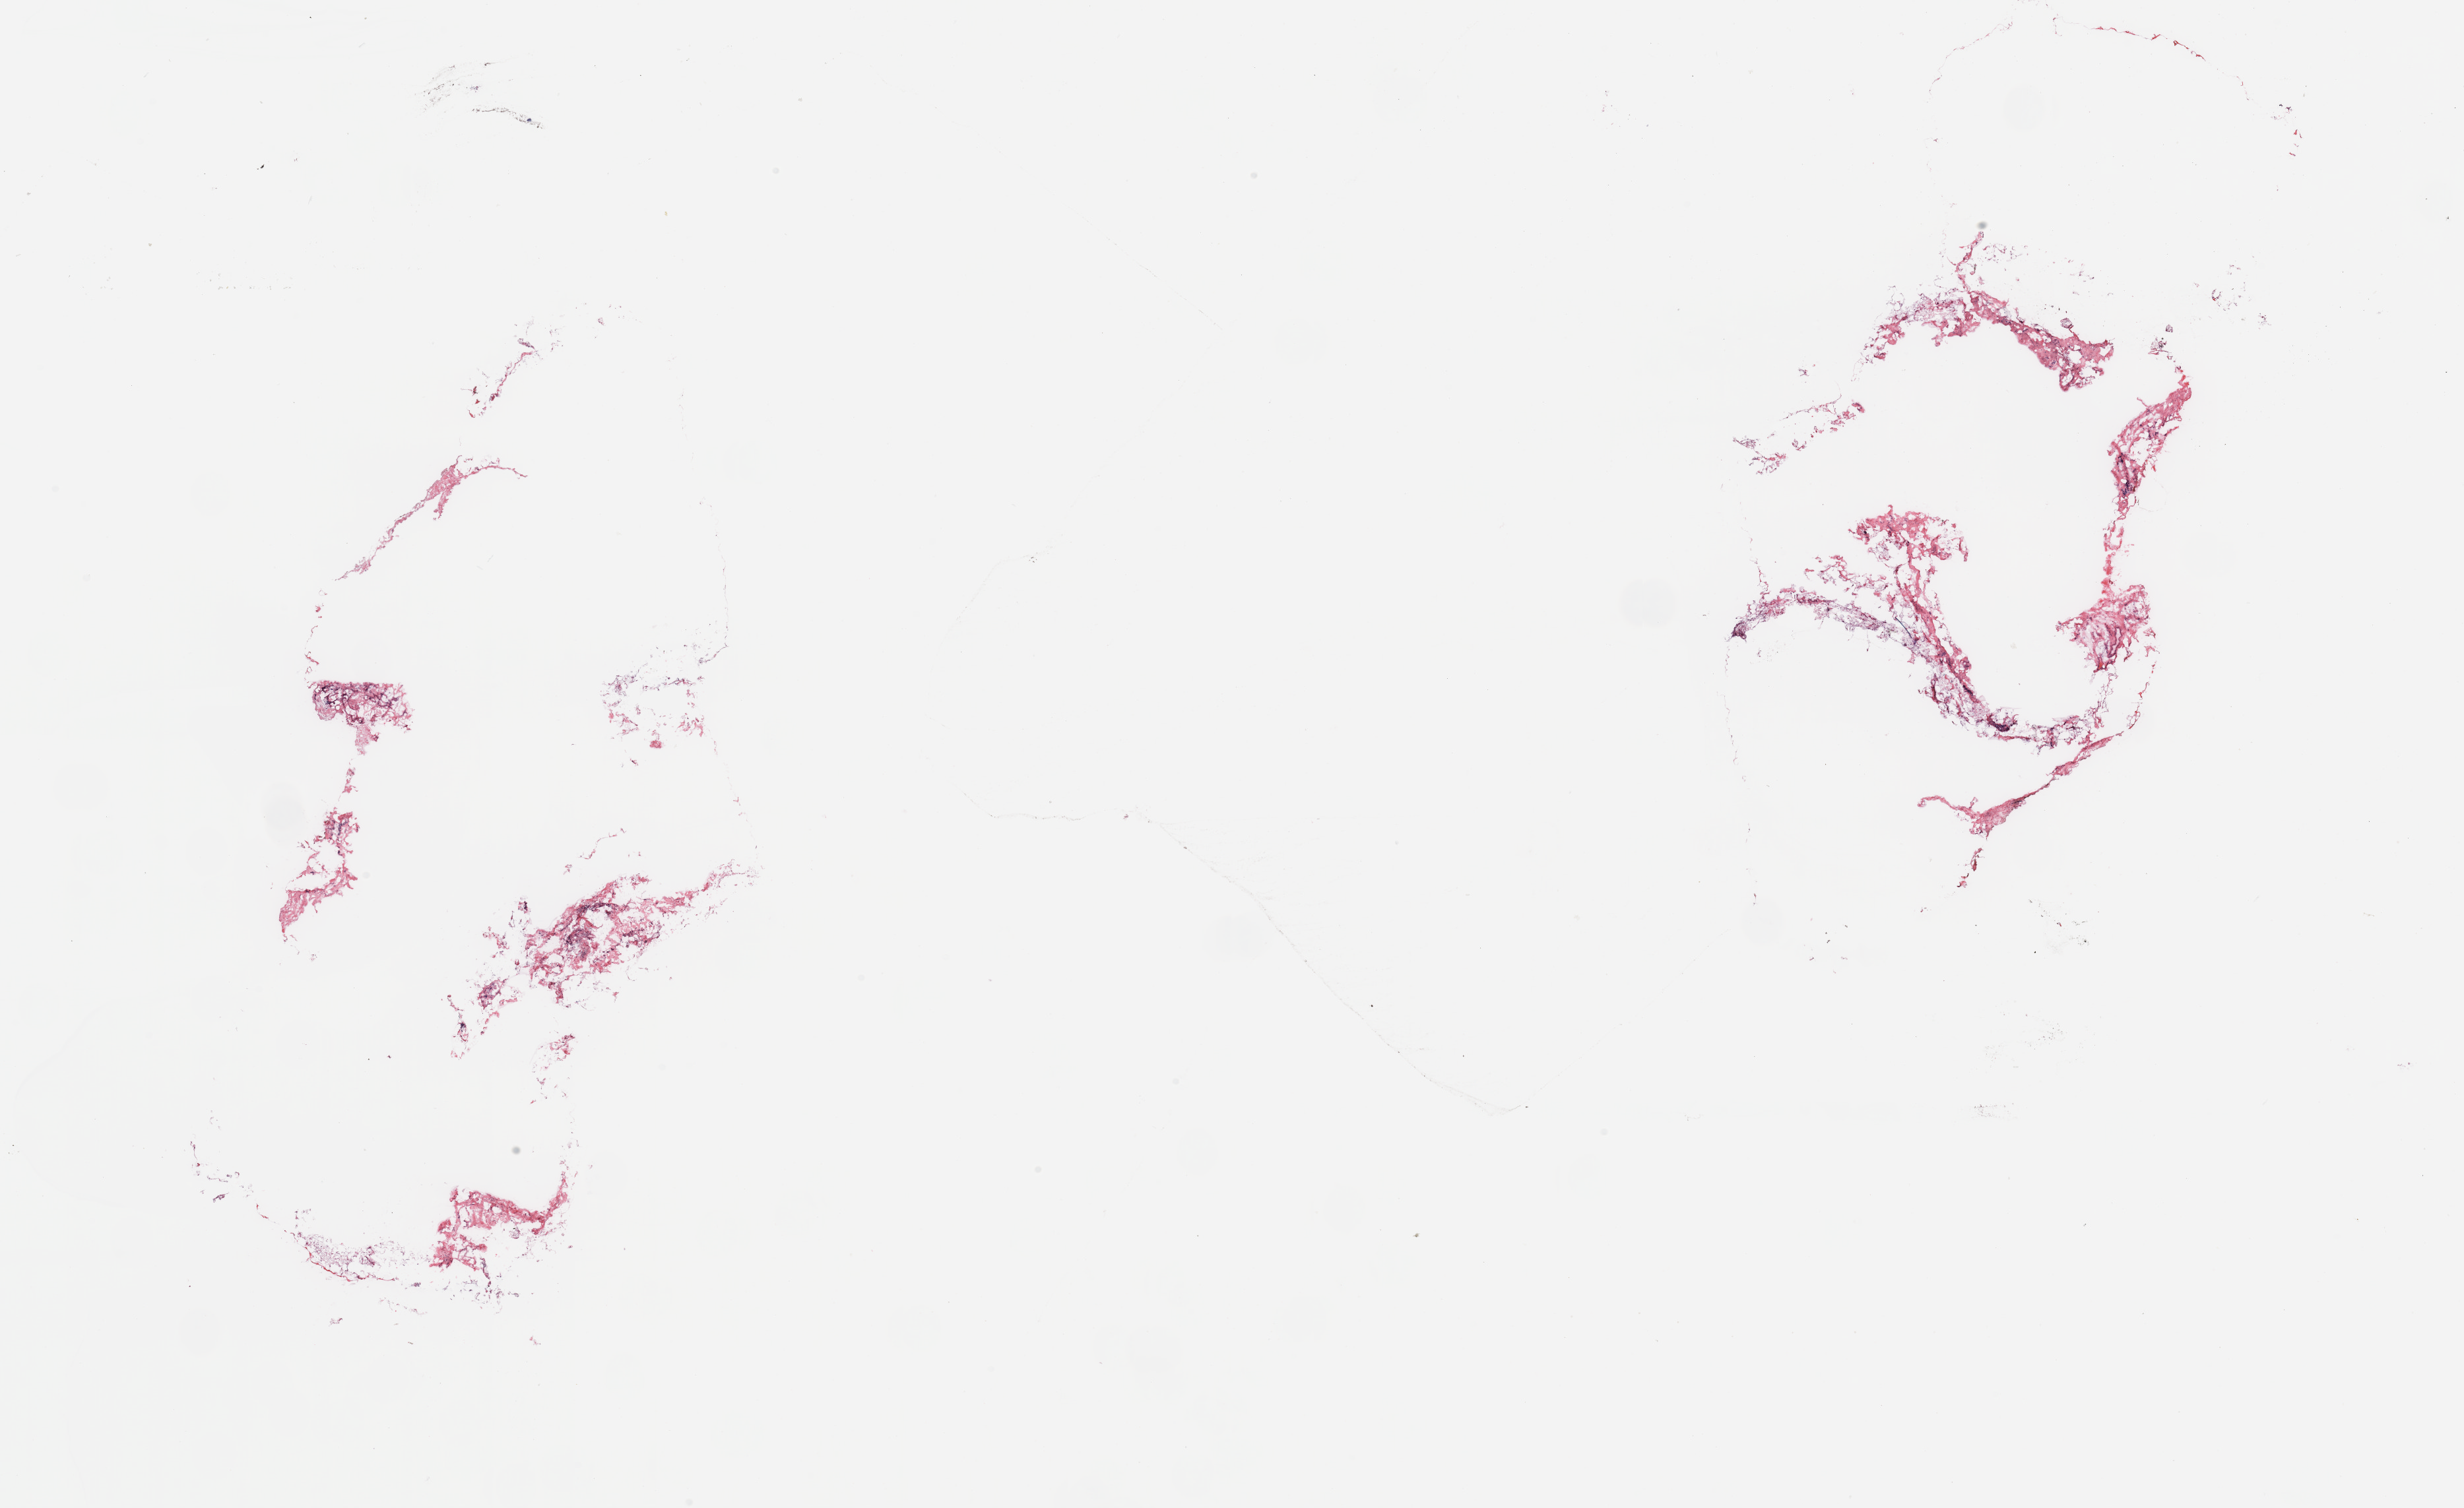
Whole-slide histology image, Hematoxylin and eosin (H&E) stained, a low-resolution overview of the entire scanned area, about 29.5 x 18.1 mm (from a 20x scan); breast, tumour tissue. 50-year-old female patient.
Diagnosis: Infiltrating duct carcinoma, NOS.